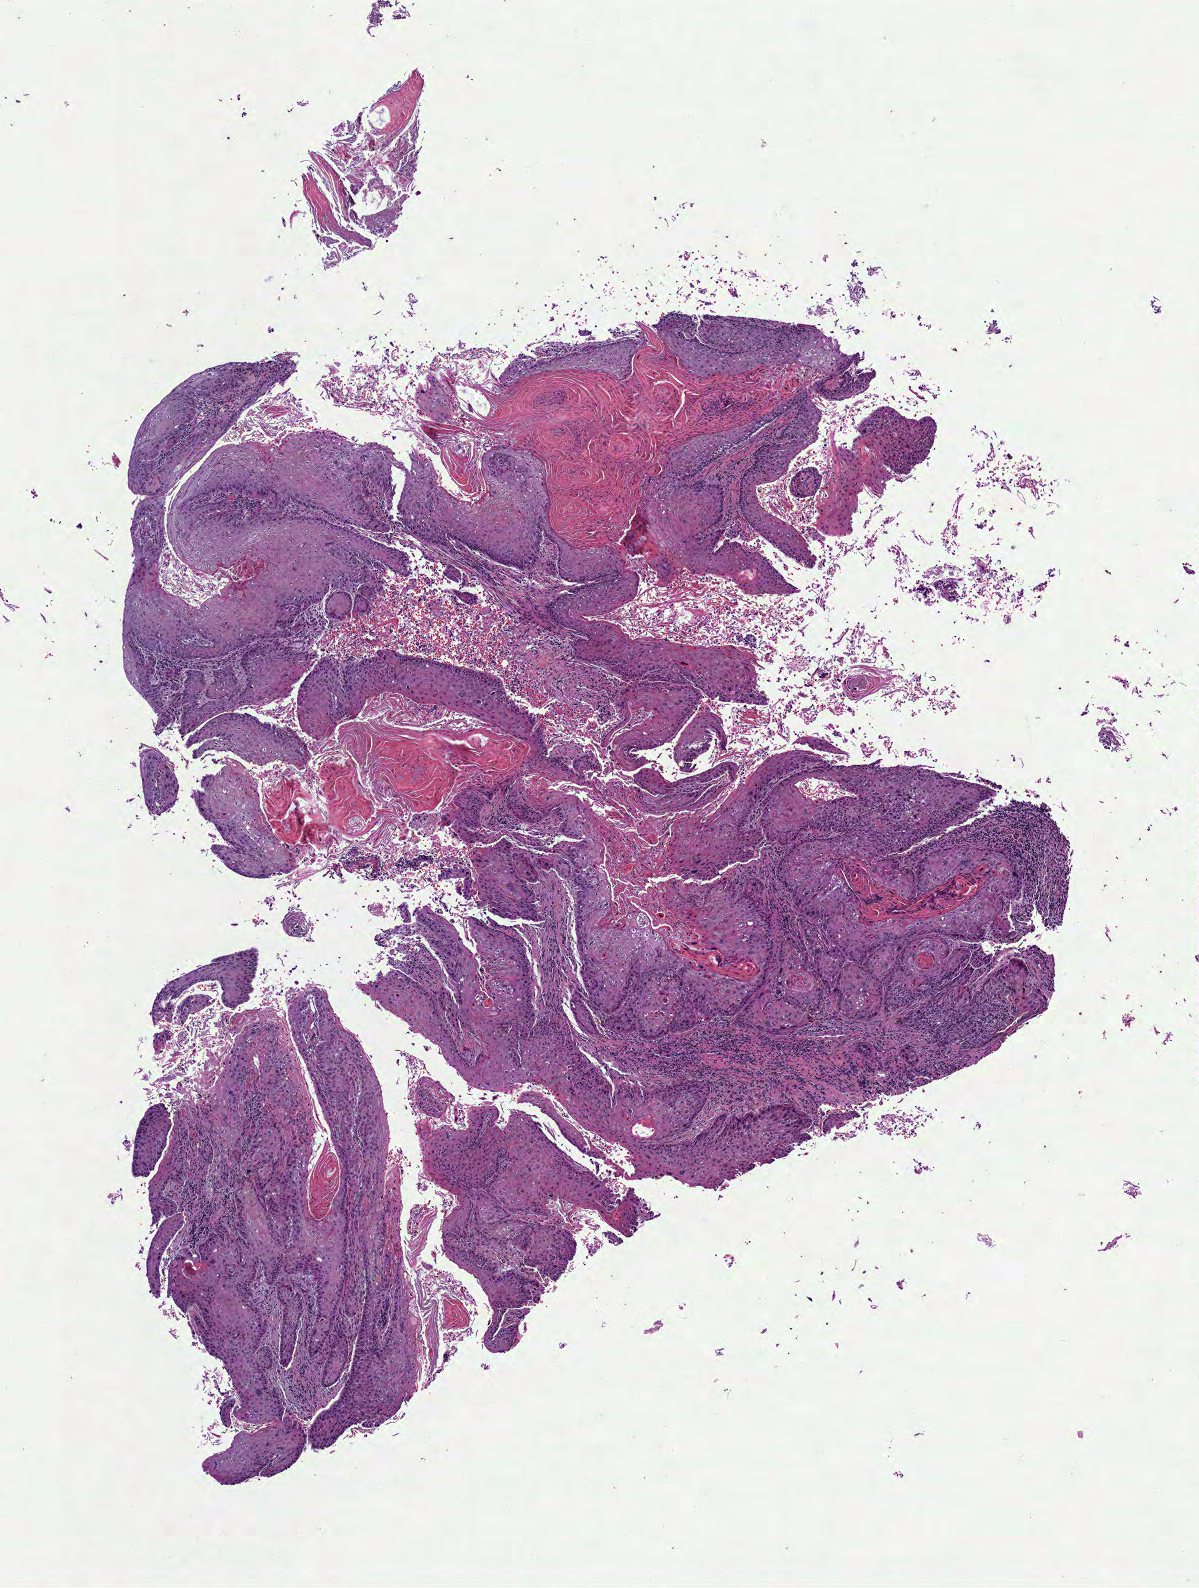
Whole-slide histology image, Hematoxylin and eosin (H&E) stained — low-resolution overview of the scanned area, about 4.8 x 6.4 mm (from a 40x scan). Formalin-fixed paraffin-embedded (FFPE) diagnostic section. Primary tumour sample from the cervix. Female, age 32 years at initial diagnosis. Histologic grade: G3 (poorly differentiated).
Diagnosis: Squamous cell carcinoma, NOS (cervix uteri). FIGO stage: IIIB.